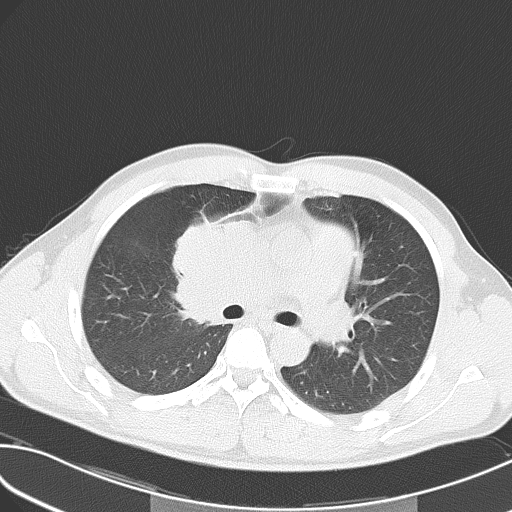
Chest CT, one axial slice. Position 34 of 55 along the scan axis. Reconstruction kernel B70f. 120 kVp. Lung window (W 1500 / L -600 HU). 5 mm slice thickness. 512 × 512 image matrix. Patient: male, 32 years. Case-level facts recorded for this patient, not image findings: clinical TNM (as recorded): T4 N3 M0; histopathological grade: G3.
Structures marked on this image (rectangle marked by the reading radiologist):
- lung tumour (recorded histology: small cell carcinoma): bounding box [x1, y1, x2, y2] px = [170, 217, 237, 331]